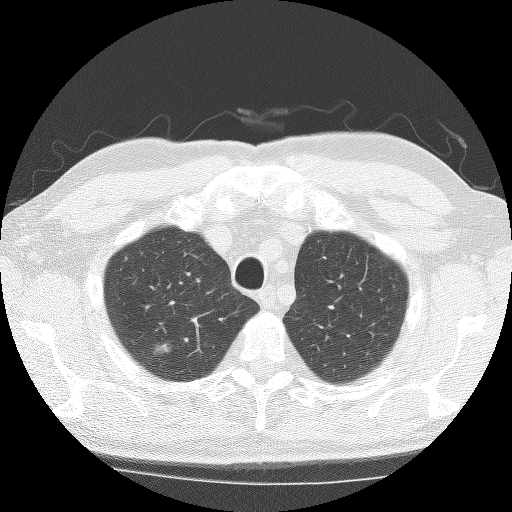
Low-dose screening chest CT, axial slice; first (baseline) screen; lung window (W 1500 / L -600 HU); 2.5 mm slice thickness; lung (sharp) reconstruction kernel (BONE); slice 15 of 38 in the series; 512 × 512 image matrix. Male, age 74 years at enrolment. Former smoker at enrolment.
Expert reader's lesion annotation, bounding box [x1, y1, x2, y2] px = [140, 331, 189, 368]. The screening reader recorded 3 non-calcified nodules or masses ≥4 mm on this exam (right upper lobe, right lower lobe, right middle lobe); which of them this box marks is not recorded.